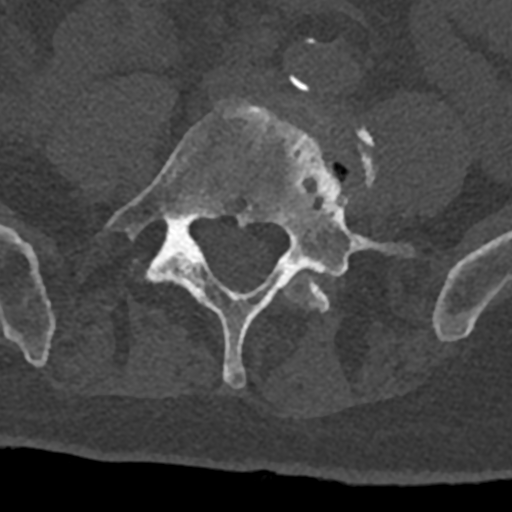
CT including the spine, one axial slice; position 210 of 797 along the scan axis; reconstruction kernel Br40s/3; bone window (W 1800 / L 400 HU); 0.5 mm slice thickness; 512 × 512 image matrix, field of view 160 × 160 mm. Male patient, age 74 years. Case-level facts recorded for this patient, not image findings: primary cancer: renal; vertebrae with lytic lesions (as recorded): T10, L1, L2, L3, L4, L5.
Annotated regions visible in this slice (semi-automatically segmented with operator editing):
- L4 vertebra: box from (x=283, y=82) to (x=377, y=313) px
- L5 vertebra: (x=105, y=100)–(x=398, y=389)